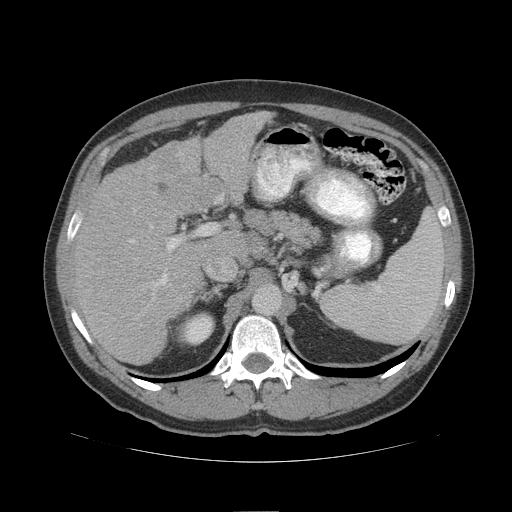
Contrast-enhanced abdominal CT (liver protocol), one axial slice. Position 66 of 109 along the scan axis. Reconstruction kernel STANDARD. Soft-tissue window (W 400 / L 40 HU). 2.5 mm slice thickness. 512 × 512 image matrix, field of view 420 × 420 mm. Case-level facts recorded for this patient, not image findings: diagnosis: hepatocellular carcinoma (patient treated with transarterial chemoembolisation; whether this scan precedes or follows treatment is not stated here); TNM stage (as recorded): Stage-IIIB; Child-Pugh class: A; tumour differentiation: poorly differentiated.
Outlined on this slice (semi-automatically segmented with operator editing):
- liver parenchyma outside the tumour (the mass and vessels are separate outlines, so this box may not span the whole liver): bounding box [x1, y1, x2, y2] px = [72, 110, 273, 364]
- mass: [142, 142, 224, 211]
- liver vessels: [130, 198, 222, 286]